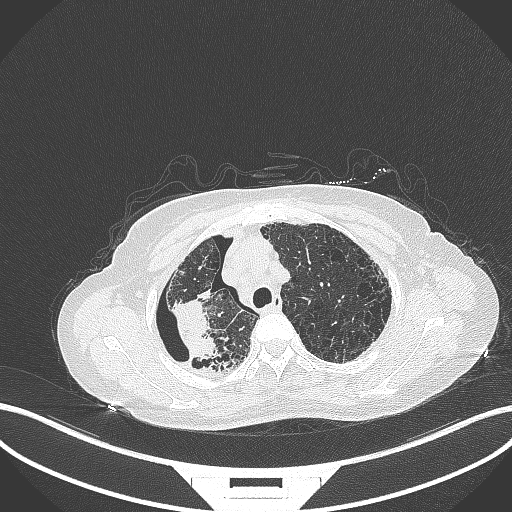
Chest CT, one axial slice; position 285 of 408 along the scan axis; lung window (W 1500 / L -600 HU); 1 mm slice thickness; 512 × 512 image matrix. Female patient, age 64 years. Case-level facts recorded for this patient, not image findings: clinical TNM (as recorded): T3 N3 M0.
Outlined on this slice (rectangle marked by the reading radiologist):
- lung tumour (recorded histology: squamous cell carcinoma): bounding box (x1, y1, x2, y2) in pixels: (160, 292, 223, 361)